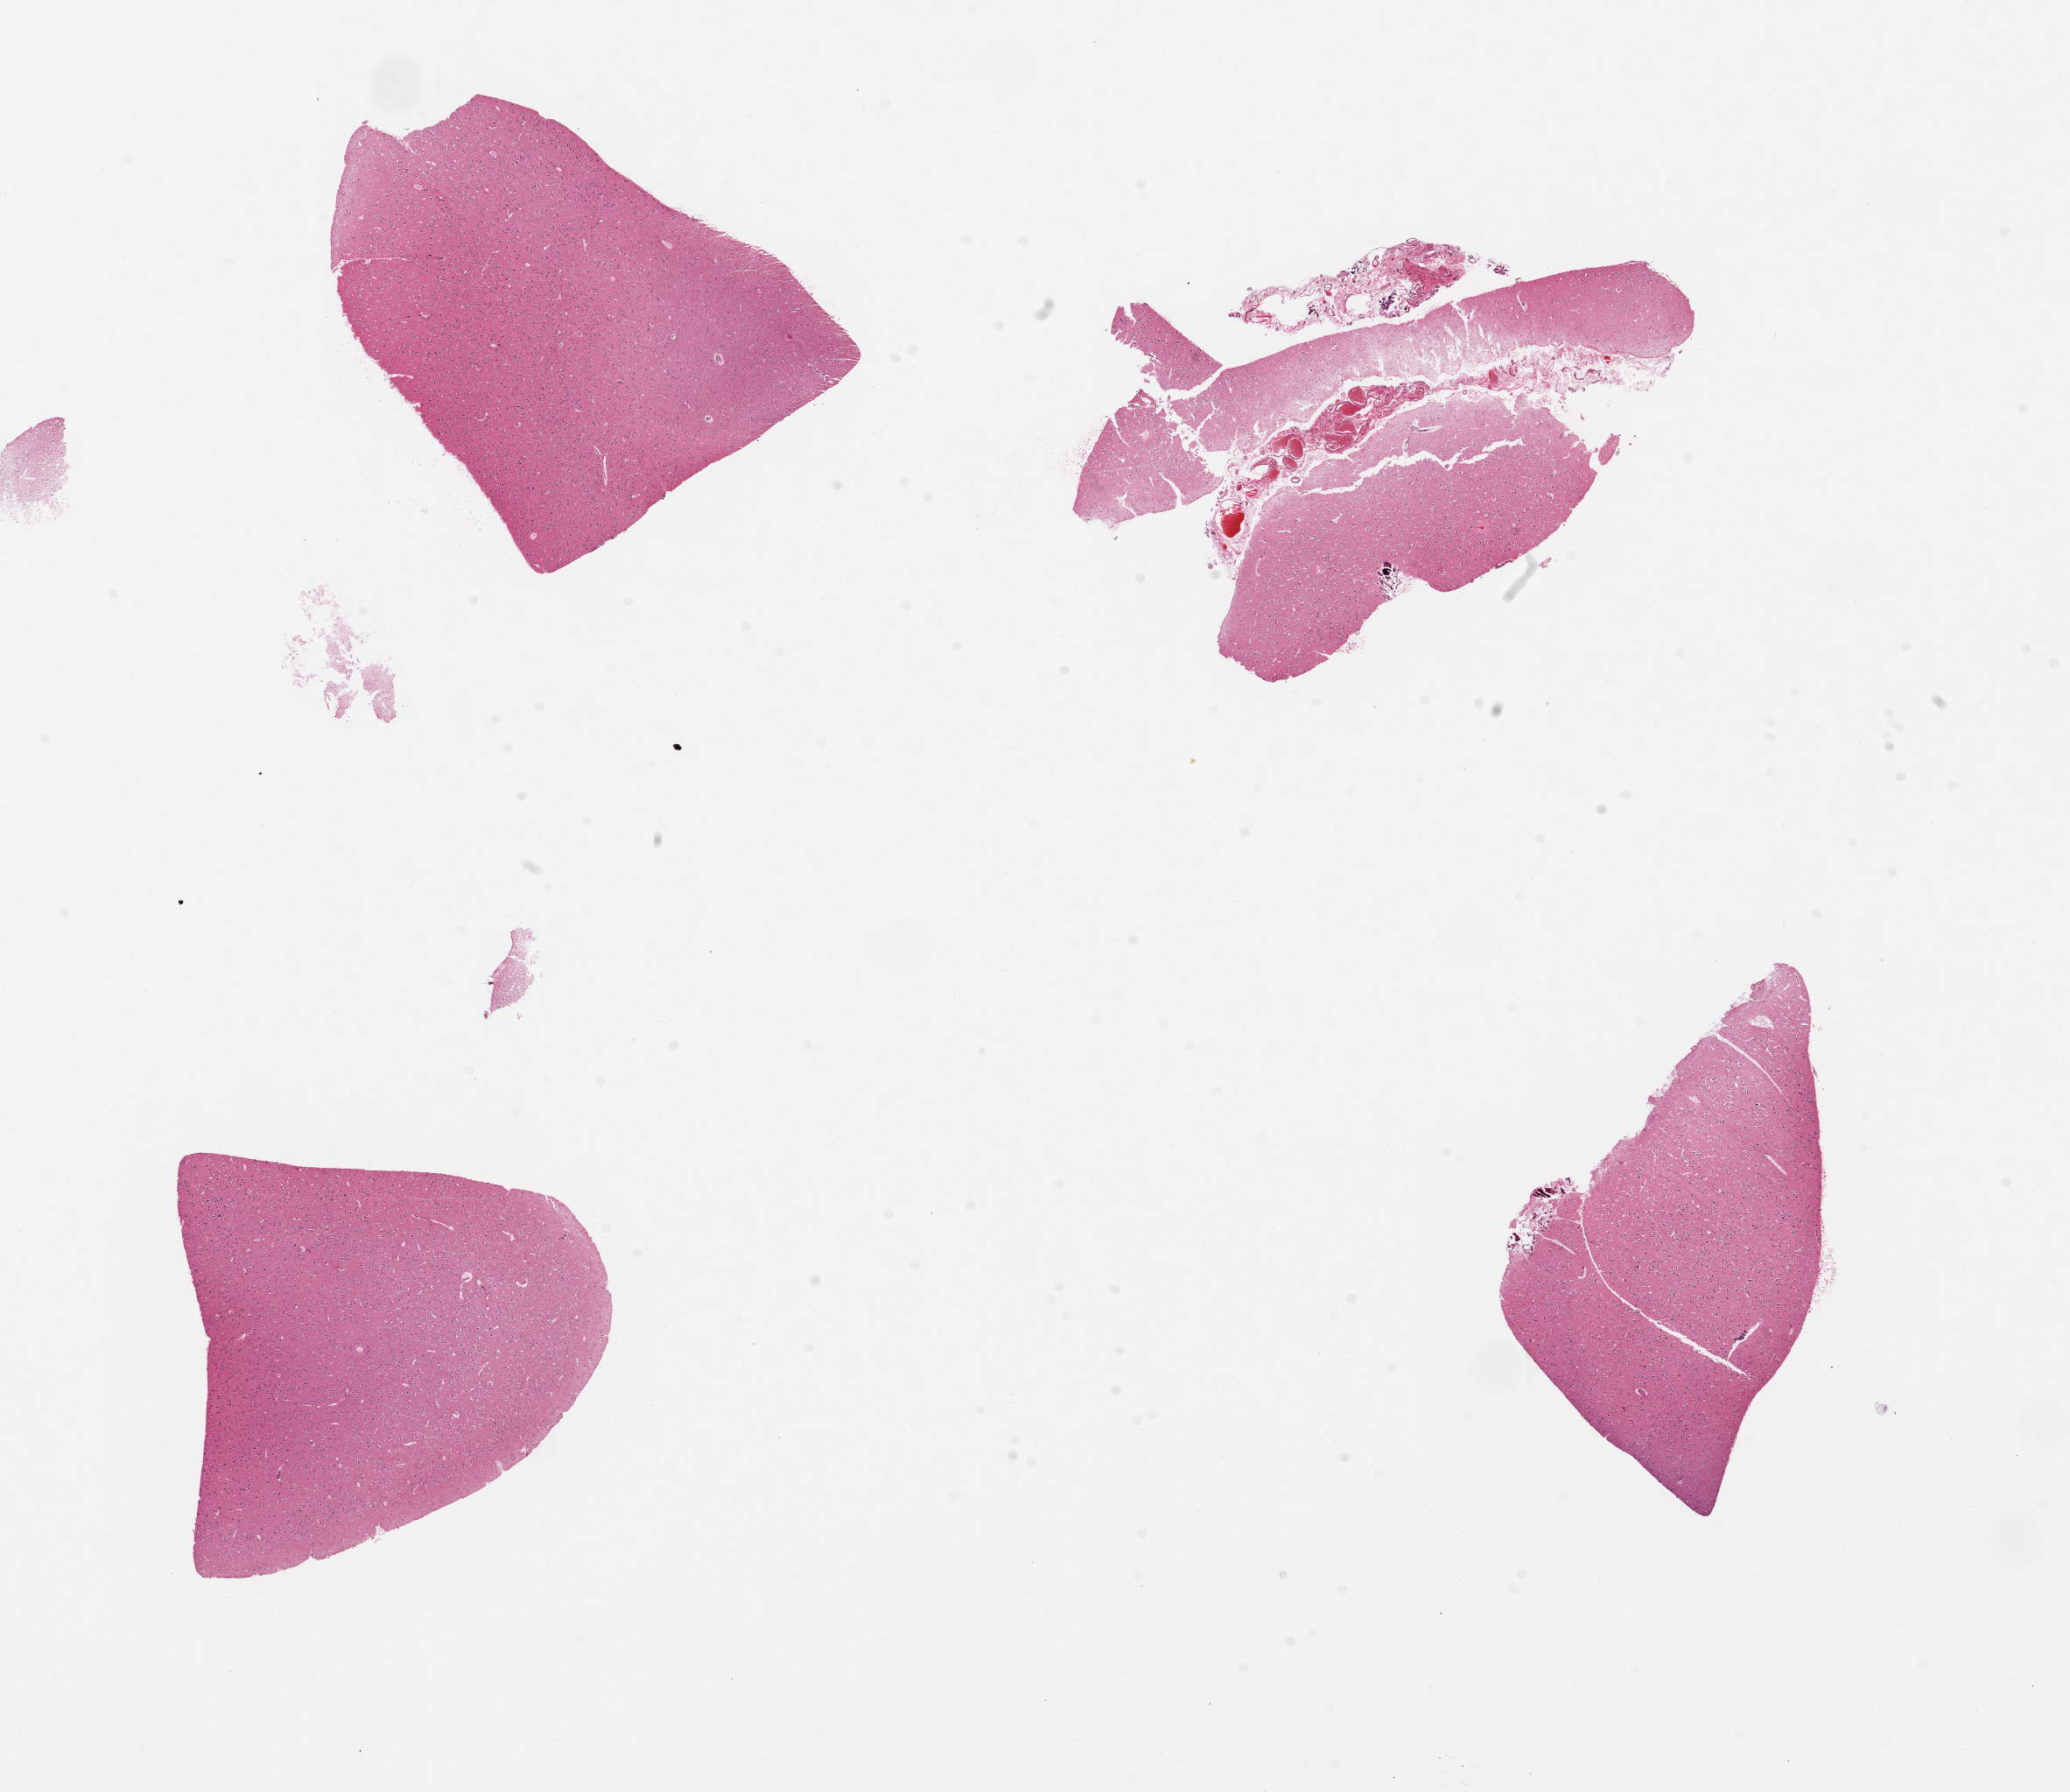
H&E whole-slide image, brightfield — shown as a low-resolution overview of the whole scanned area (about 18.7 x 16.2 mm, slide scanned at 20x). PAXgene-fixed paraffin-embedded (PFPE) section. Target tissue: cerebral cortex. Donor tissue sample. Male donor.
Review note (as recorded): 4 pieces up to 4x4 mm; one piece has meninges and vessels in a sulcus.